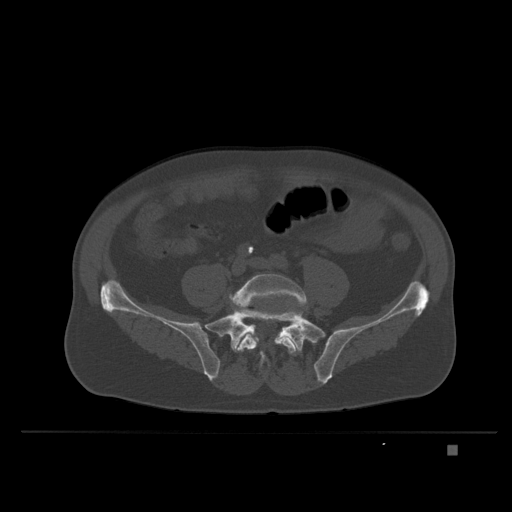
CT including the spine, one axial slice. Position 49 of 435 along the scan axis. Bone window (W 1800 / L 400 HU). 1.5 mm slice thickness. 512 × 512 image matrix, field of view 434 × 434 mm. Male patient, age 73 years. From the clinical record (not read from this slice): primary cancer: skin.
Annotated regions visible in this slice (semi-automatic segmentation, software-assisted and operator-edited):
- L5 vertebra: bounding box [x1, y1, x2, y2] px = [229, 274, 307, 368]